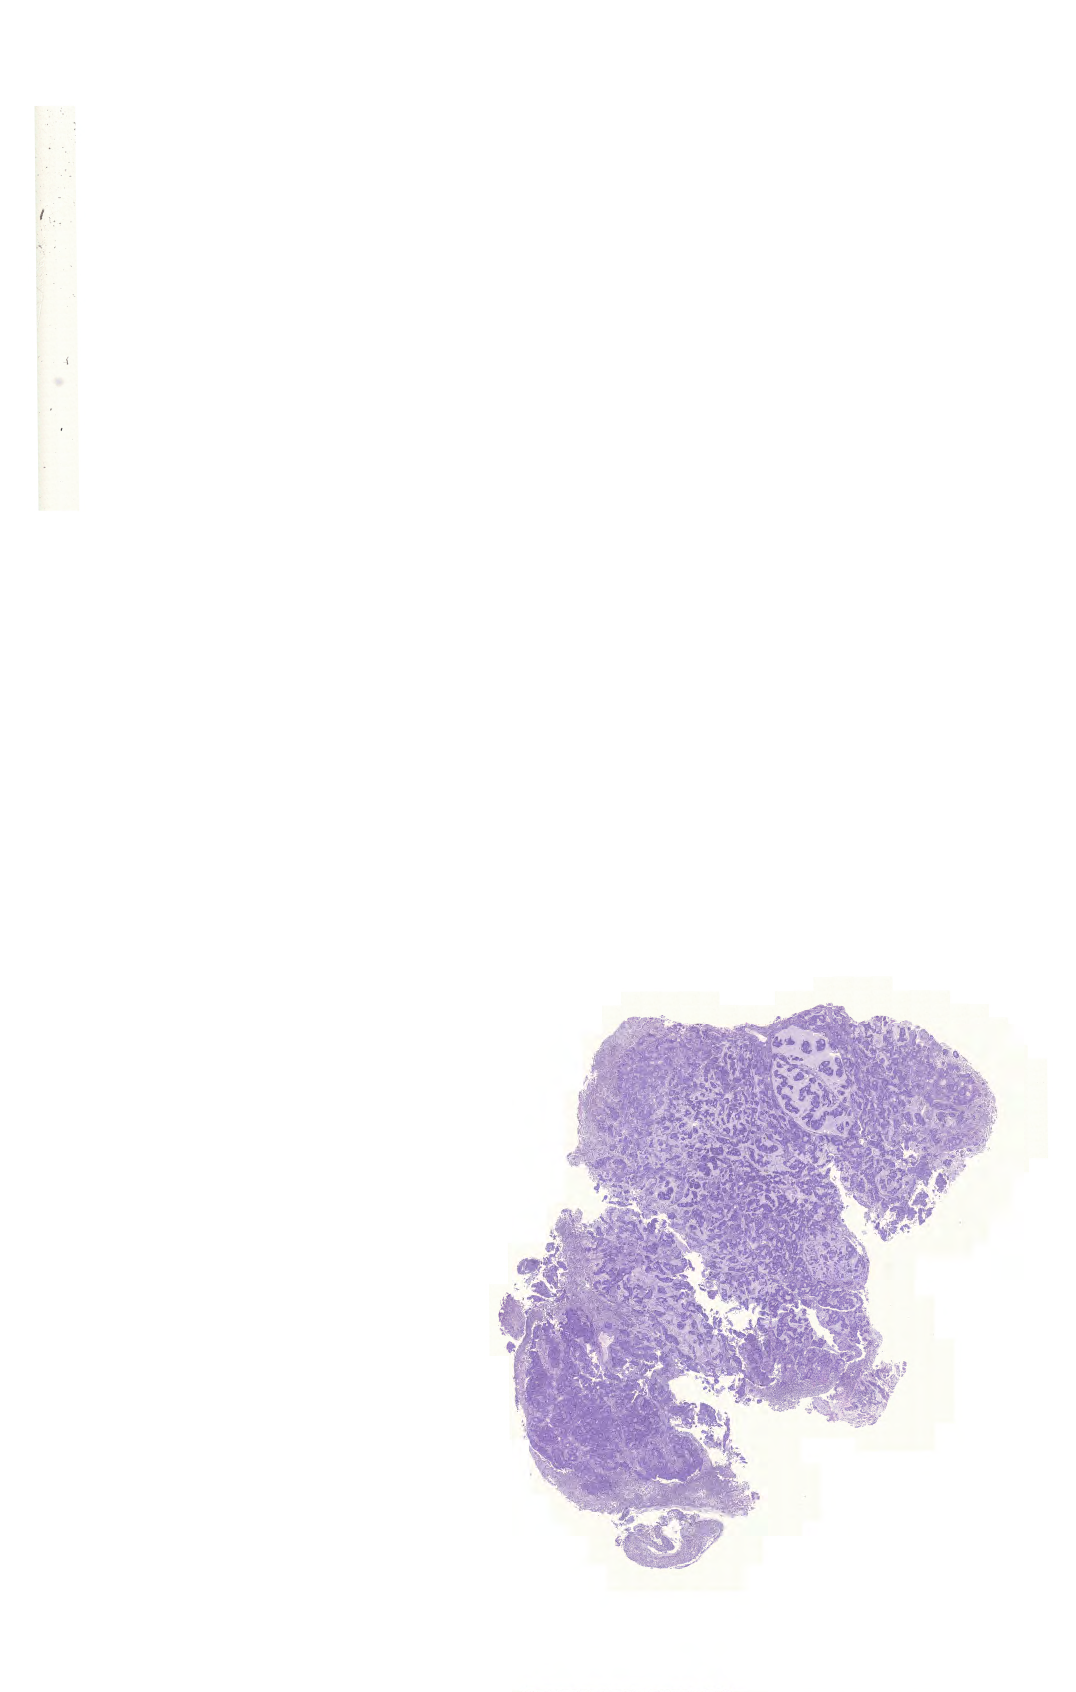
Digitized H&E-stained tissue section (whole slide) — whole scanned area (about 16.0 x 25.2 mm) shown as a low-resolution overview. Formalin-fixed paraffin-embedded (FFPE) diagnostic section. Sample: primary tumour, colon. Patient: female, age at initial diagnosis 79 years.
Pathologic diagnosis: Mucinous adenocarcinoma (ascending colon).